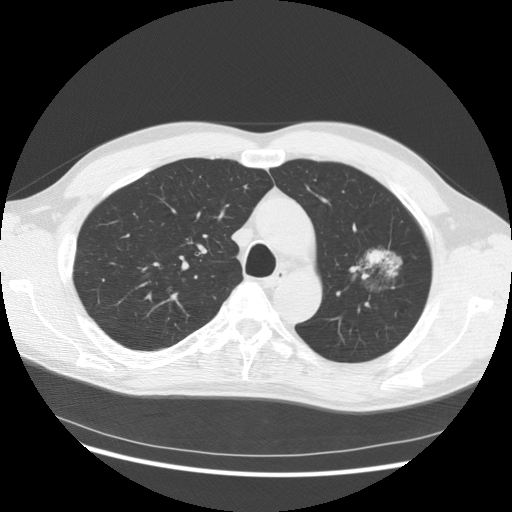
Low-dose screening chest CT, axial slice. Third annual screen. Lung window (W 1500 / L -600 HU). 2.5 mm slice thickness. Slice 102 of 145 in the series. Male, age 61 years at enrolment.
Lesion marked by an expert reader, bounding box <332,228,412,308> (left, top, right, bottom; pixels). Screening reader's record for this exam (one nodule recorded; not confirmed to be the boxed lesion): non-calcified nodule or mass ≥4 mm, left upper lobe, 37 × 33 mm, poorly defined margins, mixed attenuation, pre-existing on the prior screen: yes; interval growth: yes.